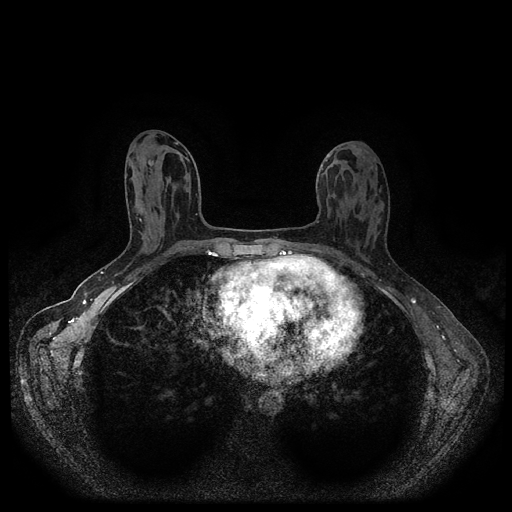
Breast MRI (dynamic contrast-enhanced, multi-phase), one axial slice. Slice 43 of 116 in the series (ordered by position). Dynamic contrast-enhanced series, time point 2 of 5 at this slice position (early post-contrast). 1.5 T. TE 2.6 ms, TR 5.4 ms. 2 mm slice thickness. 512 × 512 image matrix. Female patient, age 30 years.
Annotated regions visible in this slice (semi-automatic segmentation, software-assisted and operator-edited):
- breast lesion (labelled benign in the annotation): bounding box [x1, y1, x2, y2] px = [145, 159, 154, 170]